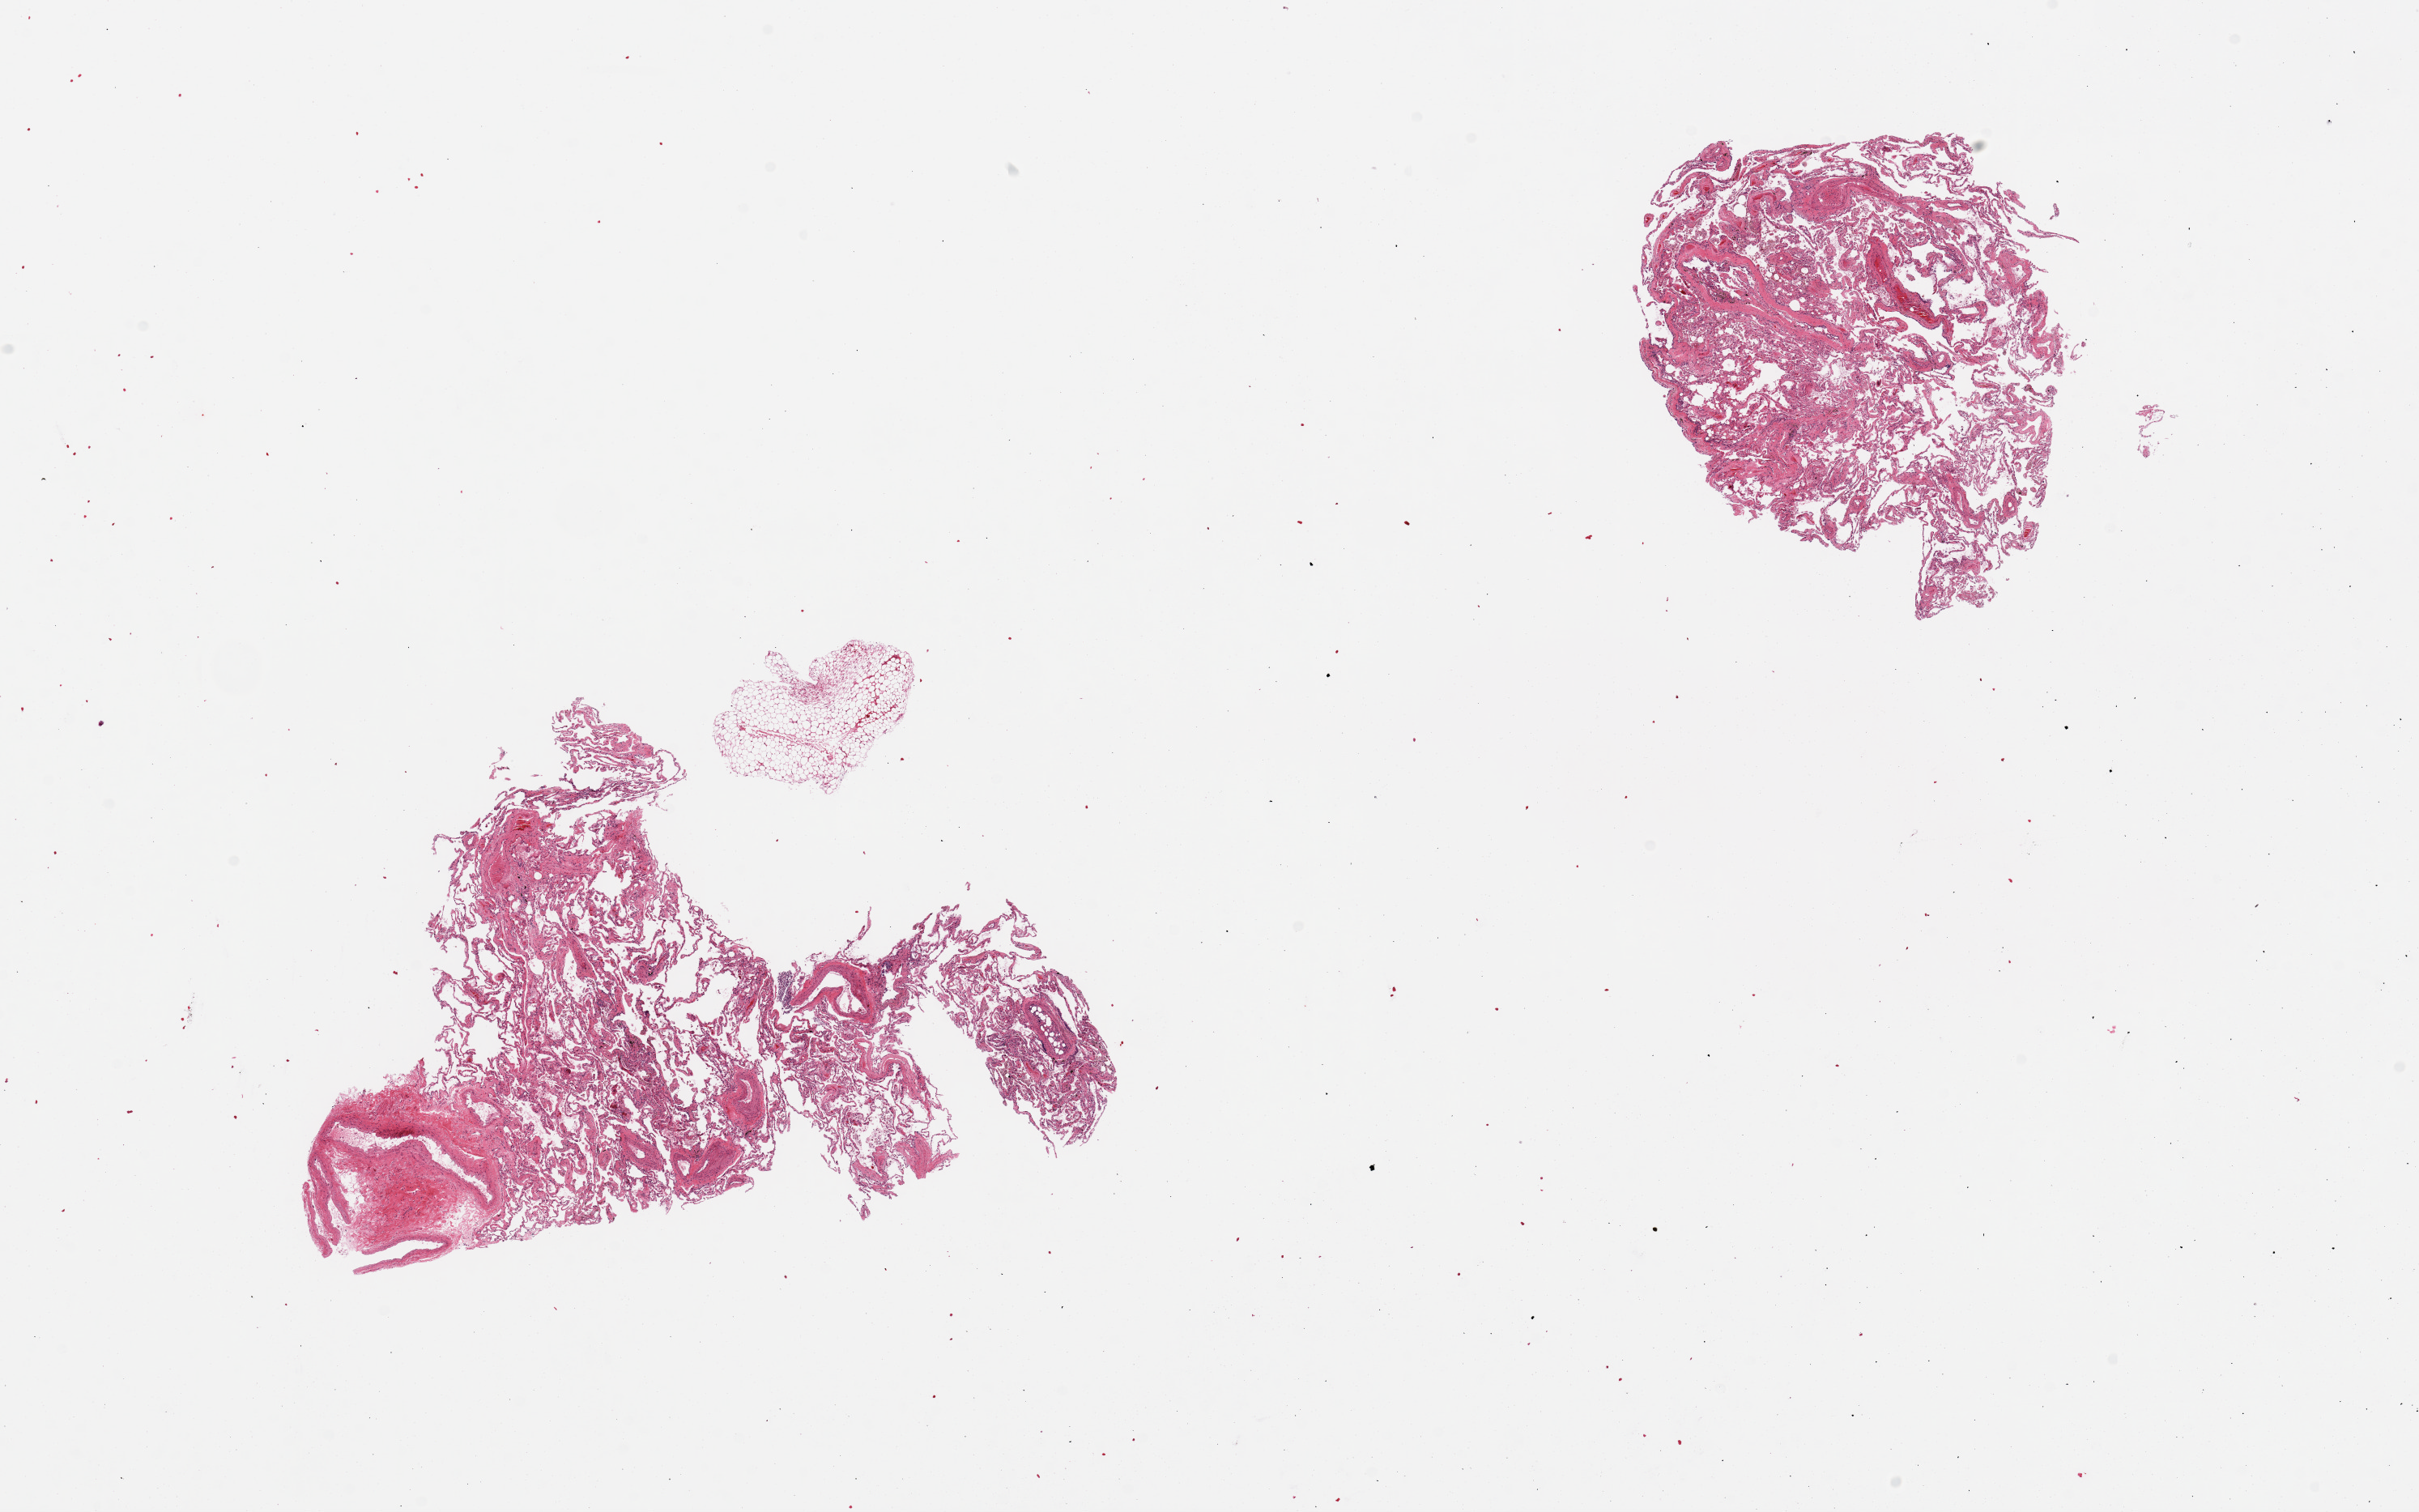
Digitized H&E-stained section — a low-resolution overview of the entire scanned area, about 23.6 x 14.8 mm; PAXgene-fixed paraffin-embedded (PFPE) section; target tissue: lung; donor tissue sample. Donor sex: female.
Reviewer comment on this tissue sample: 2 pieces, fibrin deposition in alveolar septa.